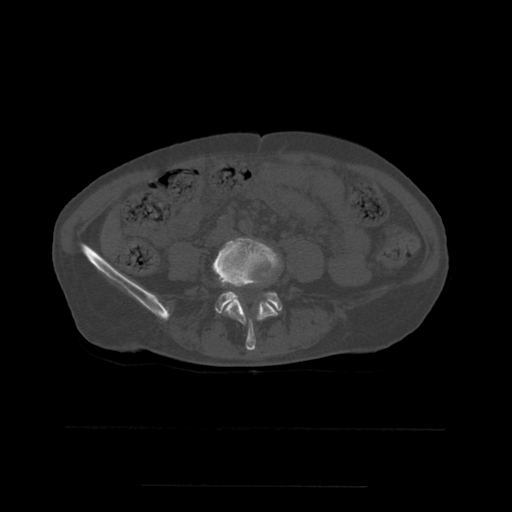
CT including the spine, one axial slice; position 158 of 544 along the scan axis; bone window (W 1800 / L 400 HU); 1.25 mm slice thickness; 512 × 512 image matrix. Patient age 58 years. Case-level facts recorded for this patient, not image findings: primary cancer: lung.
Structures marked on this image (semi-automatic segmentation, software-assisted and operator-edited):
- L4 vertebra: box from (x=215, y=238) to (x=281, y=351) px
- L5 vertebra: (x=214, y=264)–(x=282, y=314)